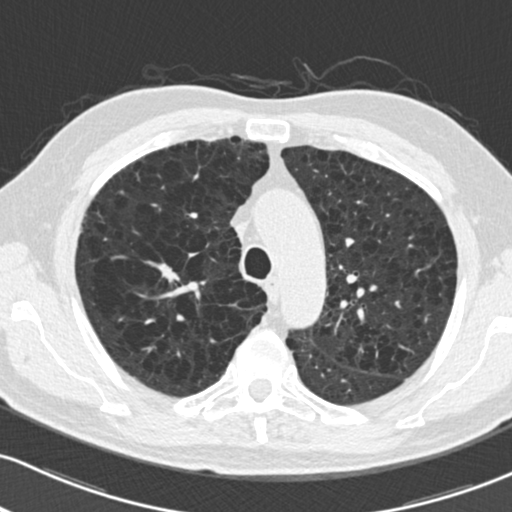
Low-dose screening chest CT, one axial slice; slice 153 of 204 in the series (ordered by position); reconstruction kernel B30f; 120 kVp; lung window (W 1500 / L -600 HU); 2 mm slice thickness; 512 × 512 image matrix.
Annotated regions visible in this slice (manually delineated by an expert):
- lesion 1 (tumor, upper lobe of right lung): bounding box (x1, y1, x2, y2) in pixels: (145, 261, 180, 283)